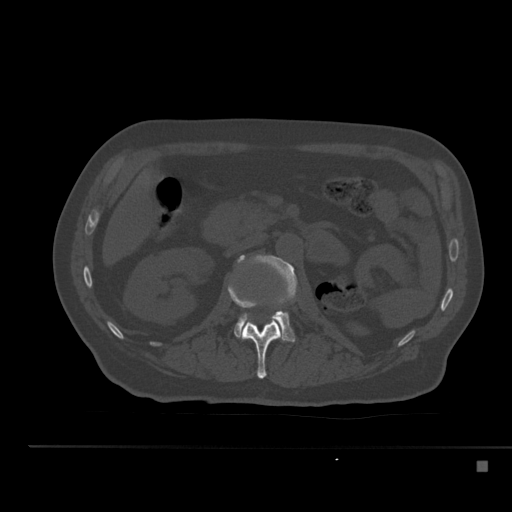
CT including the spine, one axial slice. Position 199 of 517 along the scan axis. Bone window (W 1800 / L 400 HU). 512 × 512 image matrix, field of view 408 × 408 mm. Male patient, age 70 years. Case-level facts recorded for this patient, not image findings: primary cancer: renal.
Outlined on this slice (semi-automatically segmented with operator editing):
- L1 vertebra: box from (x=228, y=283) to (x=281, y=379) px
- L2 vertebra: (x=234, y=255)–(x=297, y=341)